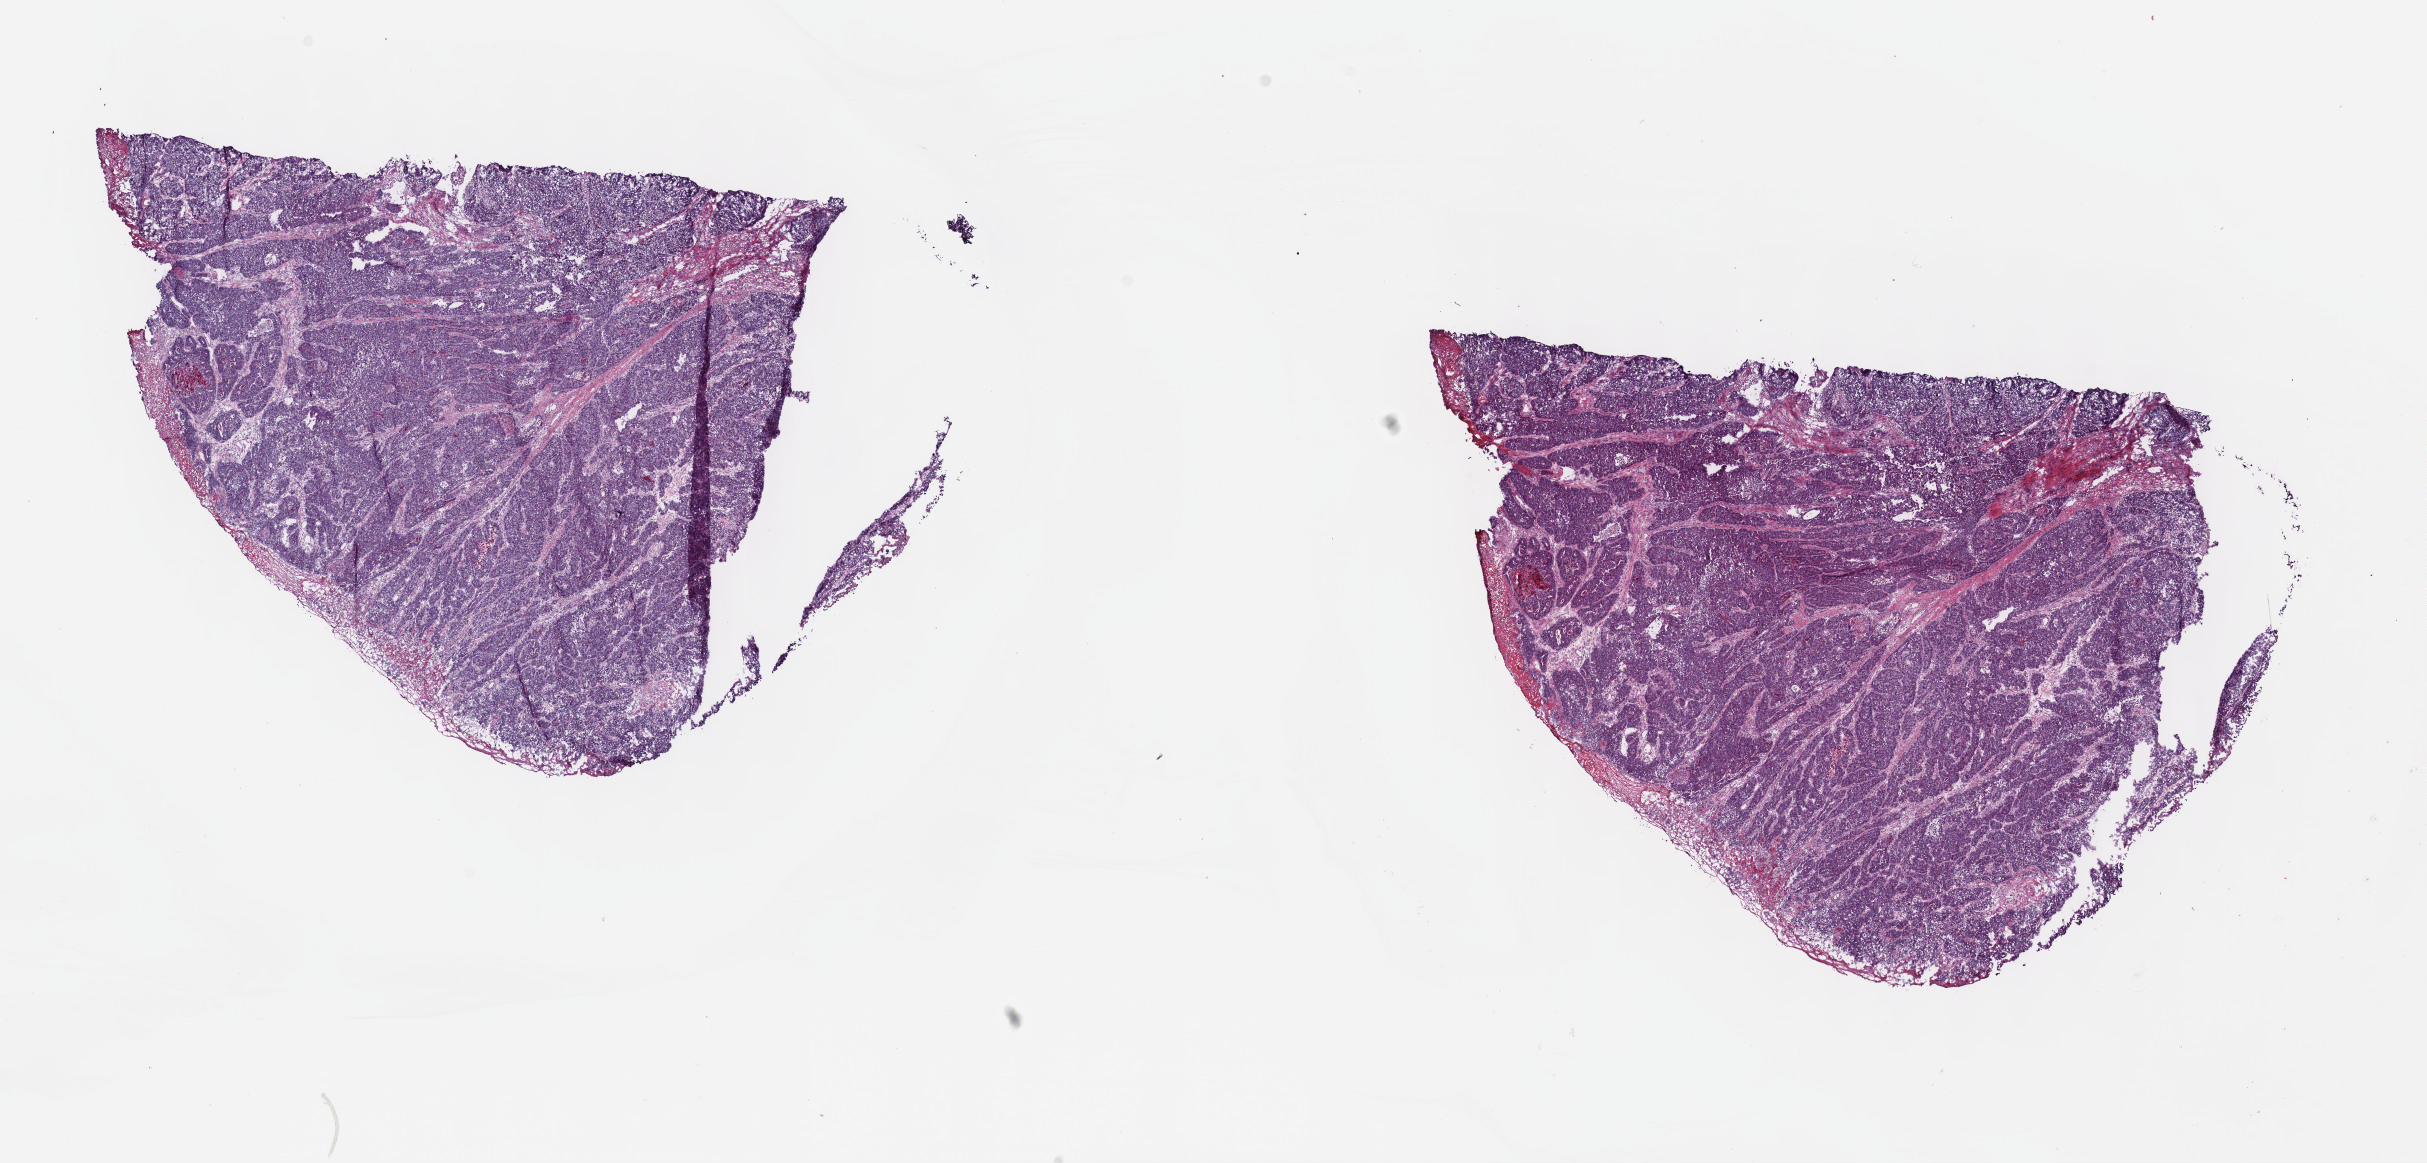
Whole-slide histology image, Hematoxylin and eosin (H&E) stained, whole scanned area (about 19.6 x 9.4 mm) shown as a low-resolution overview, frozen section from the top of the tissue portion, esophagus, primary tumour sample. Patient: male, age at initial diagnosis 51 years. Histologic grade: GX (grade cannot be assessed). Pathologist review of this section (percent, as recorded): tumour cells 90%, tumour nuclei 95%, normal cells 0%, stromal cells 10%, necrosis 0%. Infiltration values recorded for this section: lymphocyte infiltration 0%, monocyte infiltration 0%, neutrophil infiltration 0%.
Lymph nodes positive (case pathology): 2 of 30 examined. Histologic diagnosis: Adenocarcinoma, NOS (lower third of esophagus).